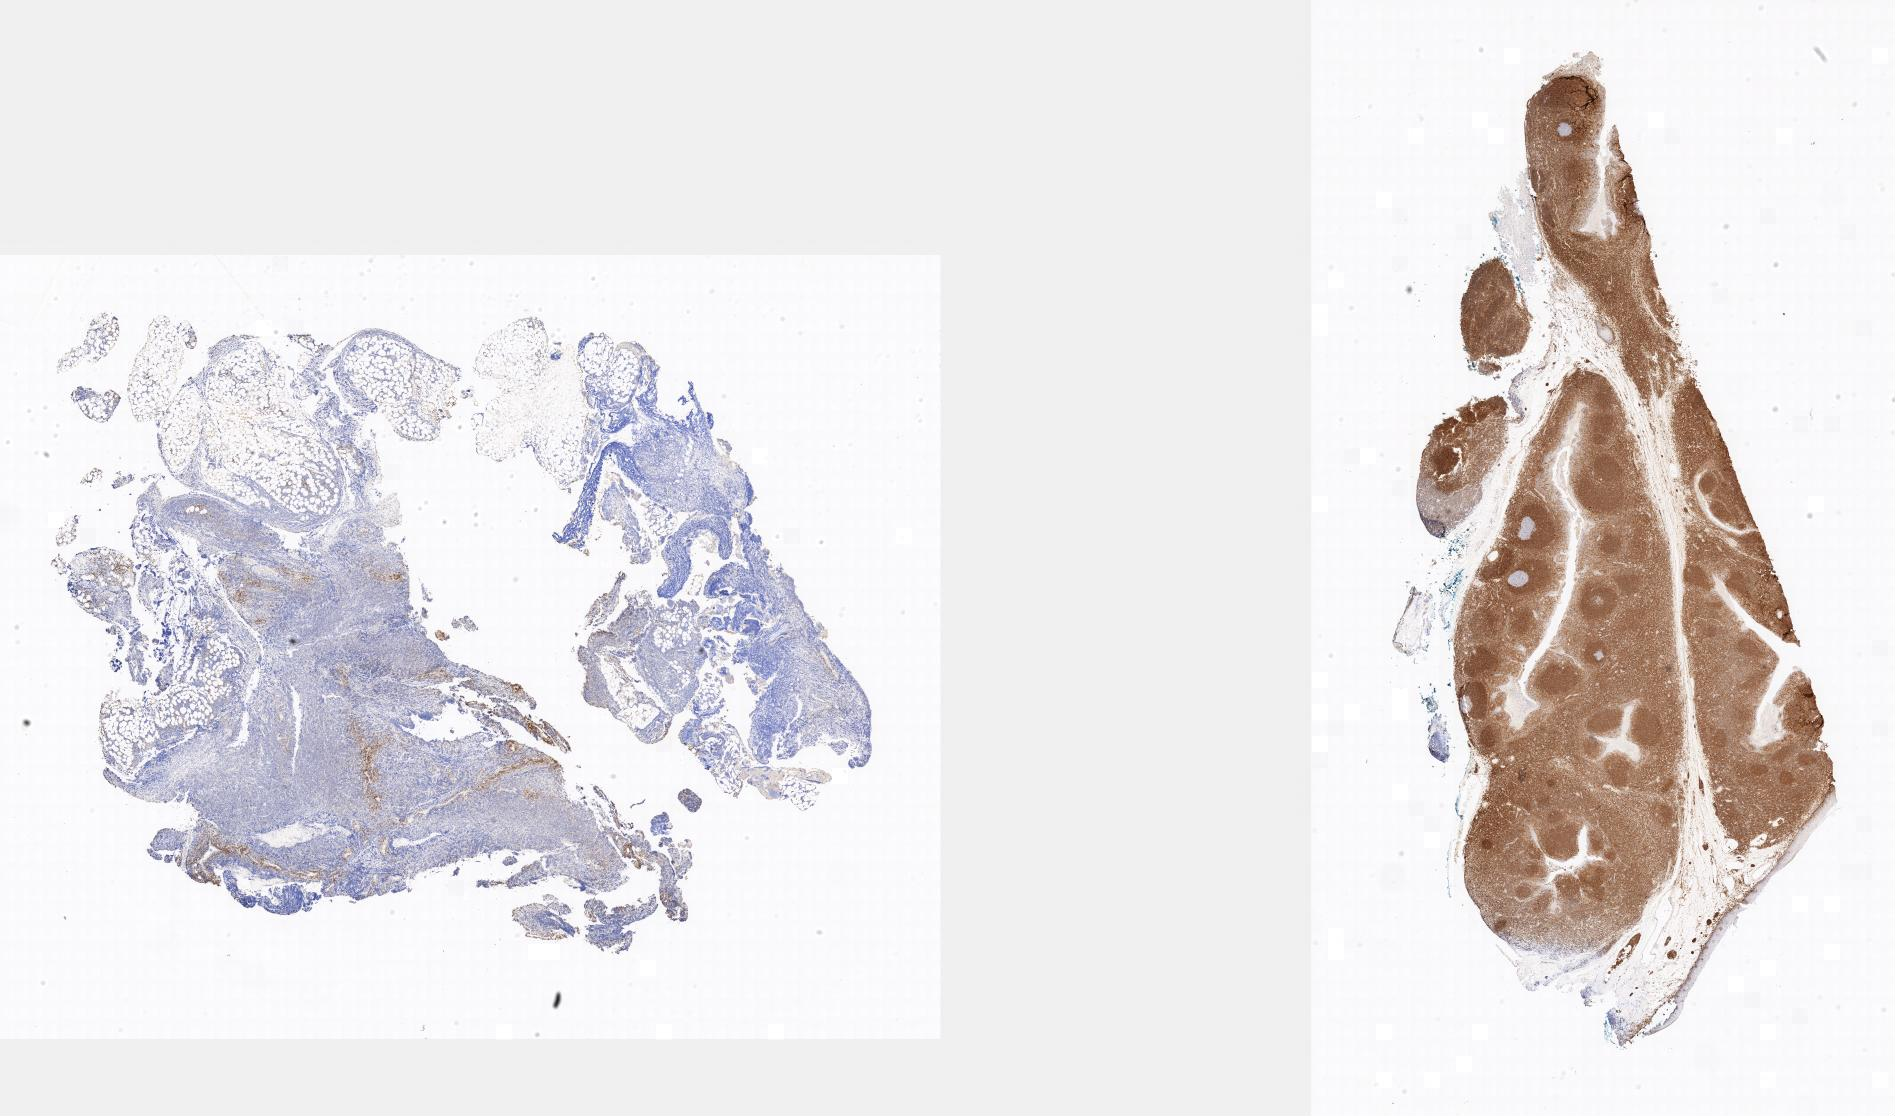
Whole-slide image, immunohistochemical stain for BCL2 — a low-resolution overview of the entire scanned area; tumor tissue; anatomic site: abdominal lymph node. Patient: male, age at initial diagnosis 9 years.
Diagnosis: Burkitt lymphoma, NOS.